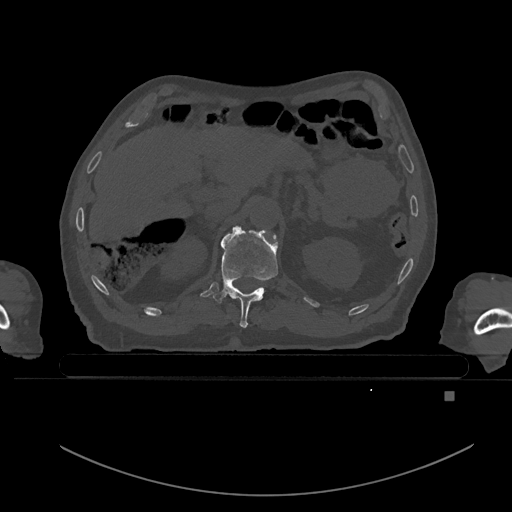
CT including the spine, one axial slice; slice 17 of 969 in the series (ordered by position); bone window (W 1800 / L 400 HU); 512 × 512 image matrix, field of view 456 × 456 mm. Patient: male, 82 years. Case-level facts recorded for this patient, not image findings: primary cancer: prostate; vertebrae with lytic lesions (as recorded): T11, T9, T8, T2.
Structures marked on this image (semi-automatic segmentation, software-assisted and operator-edited):
- T11 vertebra: bounding box <213,228,278,328> (left, top, right, bottom; pixels)